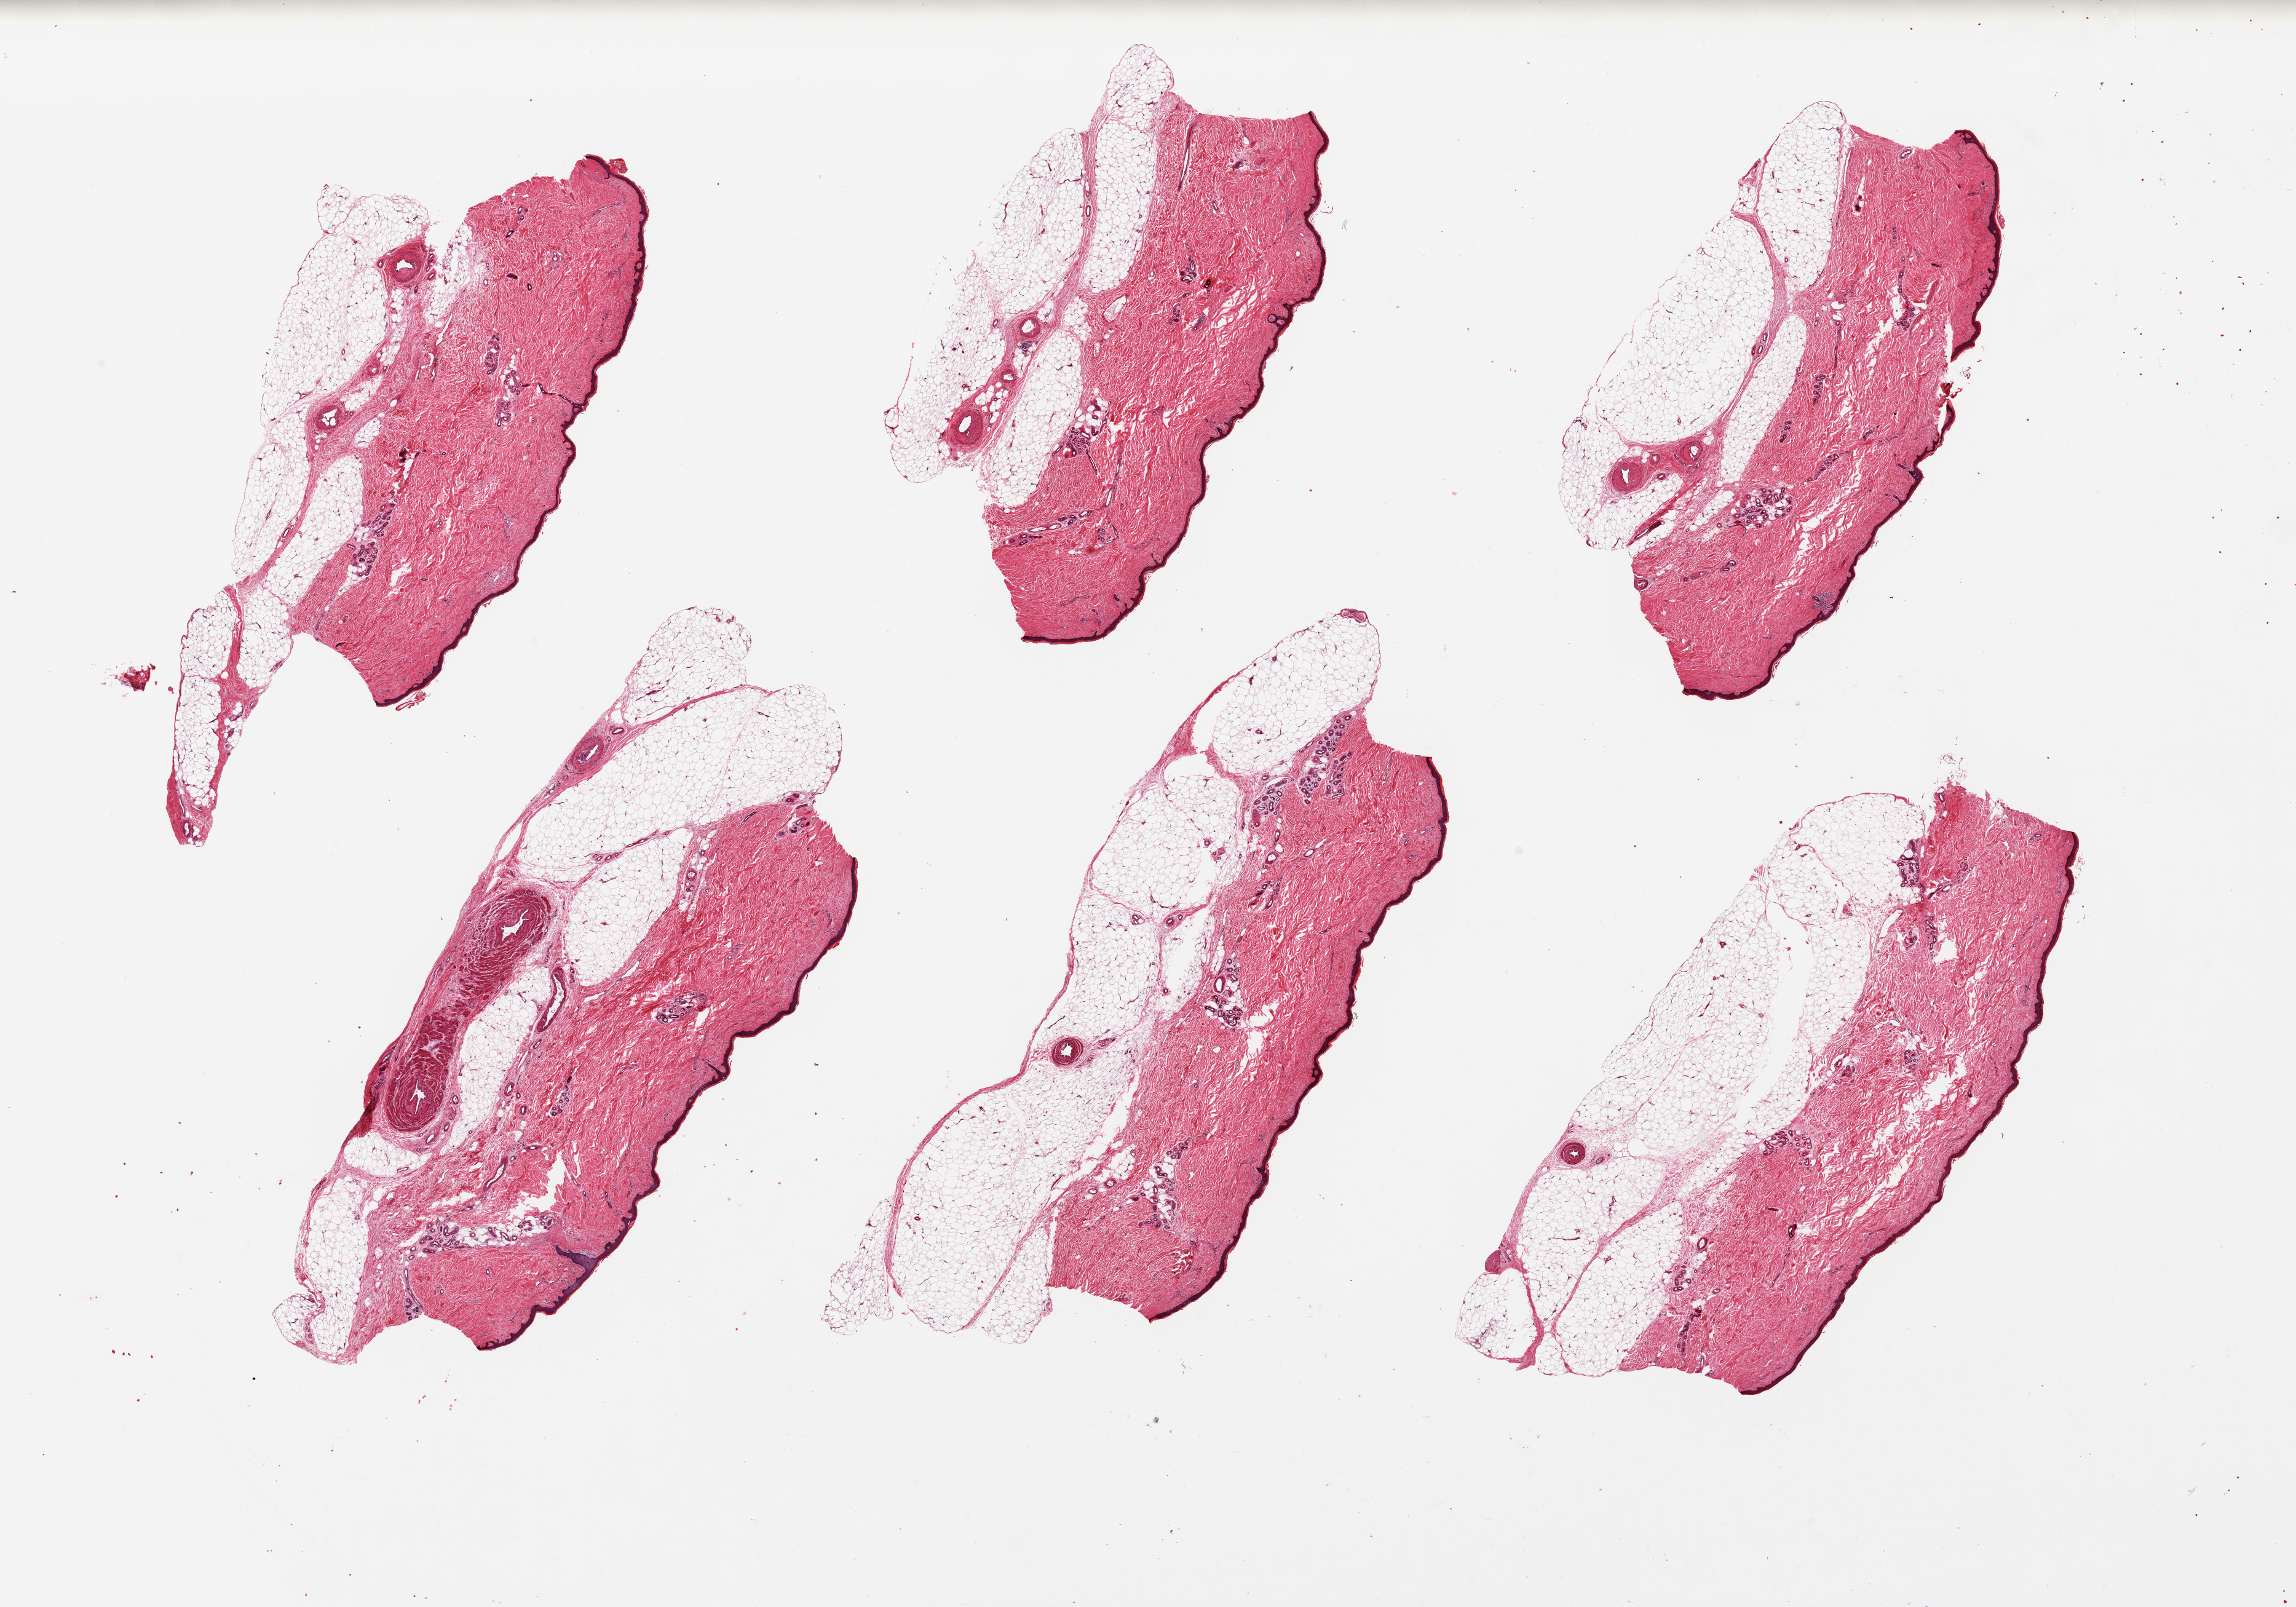
Hematoxylin and eosin (H&E) whole-slide image — low-resolution overview of the scanned area, about 29.5 x 20.7 mm (acquisition: 20x scan), PAXgene-fixed paraffin-embedded (PFPE) section, section of skin of lower leg (target tissue), tissue donor sample. Male donor.
- pathologist's review note for this sample: 6 pieces. All 6 are poorly trimmed with up to 2.5 mm of subcutaneous fat (half the total thickness of the specimen)